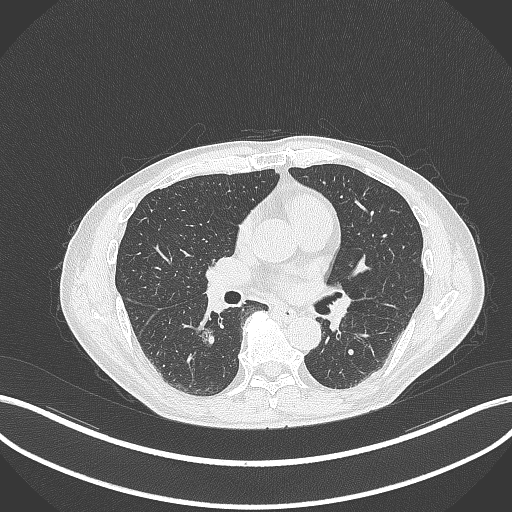
Chest CT, one axial slice; position 164 of 323 along the scan axis; reconstruction kernel B70f; lung window (W 1500 / L -600 HU); 1 mm slice thickness; 512 × 512 image matrix, field of view 400 × 400 mm. Male patient, age 61 years. From the clinical record (not read from this slice): clinical TNM (as recorded): T1c N0 M0.
Annotated regions visible in this slice (rectangle marked by the reading radiologist):
- lung tumour (recorded histology: adenocarcinoma): bounding box [x1, y1, x2, y2] px = [200, 327, 217, 351]